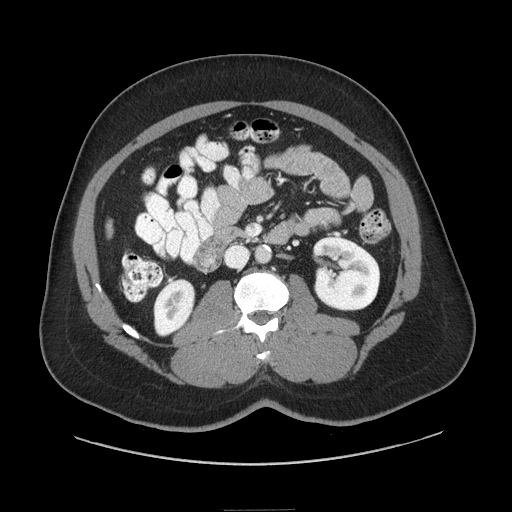
Contrast-enhanced abdominal CT (liver protocol), one axial slice. Position 15 of 87 along the scan axis. Reconstruction kernel STANDARD. 140 kVp. Soft-tissue window (W 400 / L 40 HU). 2.5 mm slice thickness. 512 × 512 image matrix, field of view 440 × 440 mm. Case-level facts recorded for this patient, not image findings: diagnosis: hepatocellular carcinoma (patient treated with transarterial chemoembolisation; whether this scan precedes or follows treatment is not stated here); TNM stage (as recorded): Stage-II; Child-Pugh class: A; tumour differentiation: moderately differentiated; tumour nodularity: uninodular.
Outlined on this slice (semi-automatic segmentation, software-assisted and operator-edited):
- liver parenchyma outside the tumour (the mass and vessels are separate outlines, so this box may not span the whole liver): bounding box [x1, y1, x2, y2] px = [106, 222, 112, 237]